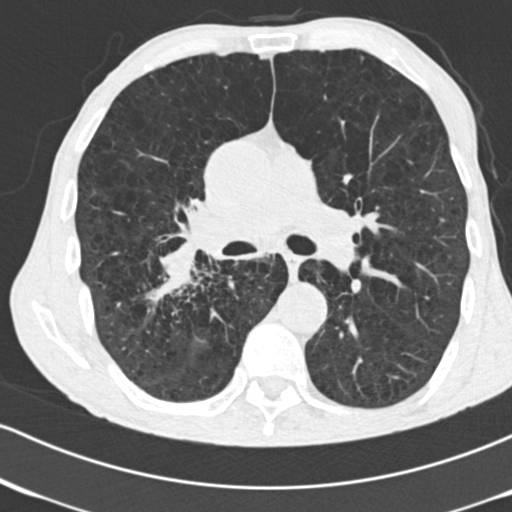
Low-dose screening chest CT, one axial slice; position 100 of 182 along the scan axis; 120 kVp; lung window (W 1500 / L -600 HU); 2 mm slice thickness; 512 × 512 image matrix, field of view 316 × 316 mm.
Annotated regions visible in this slice (expert manual segmentation):
- lesion 1 (tumor, lower lobe of right lung): box from (x=161, y=243) to (x=198, y=286) px